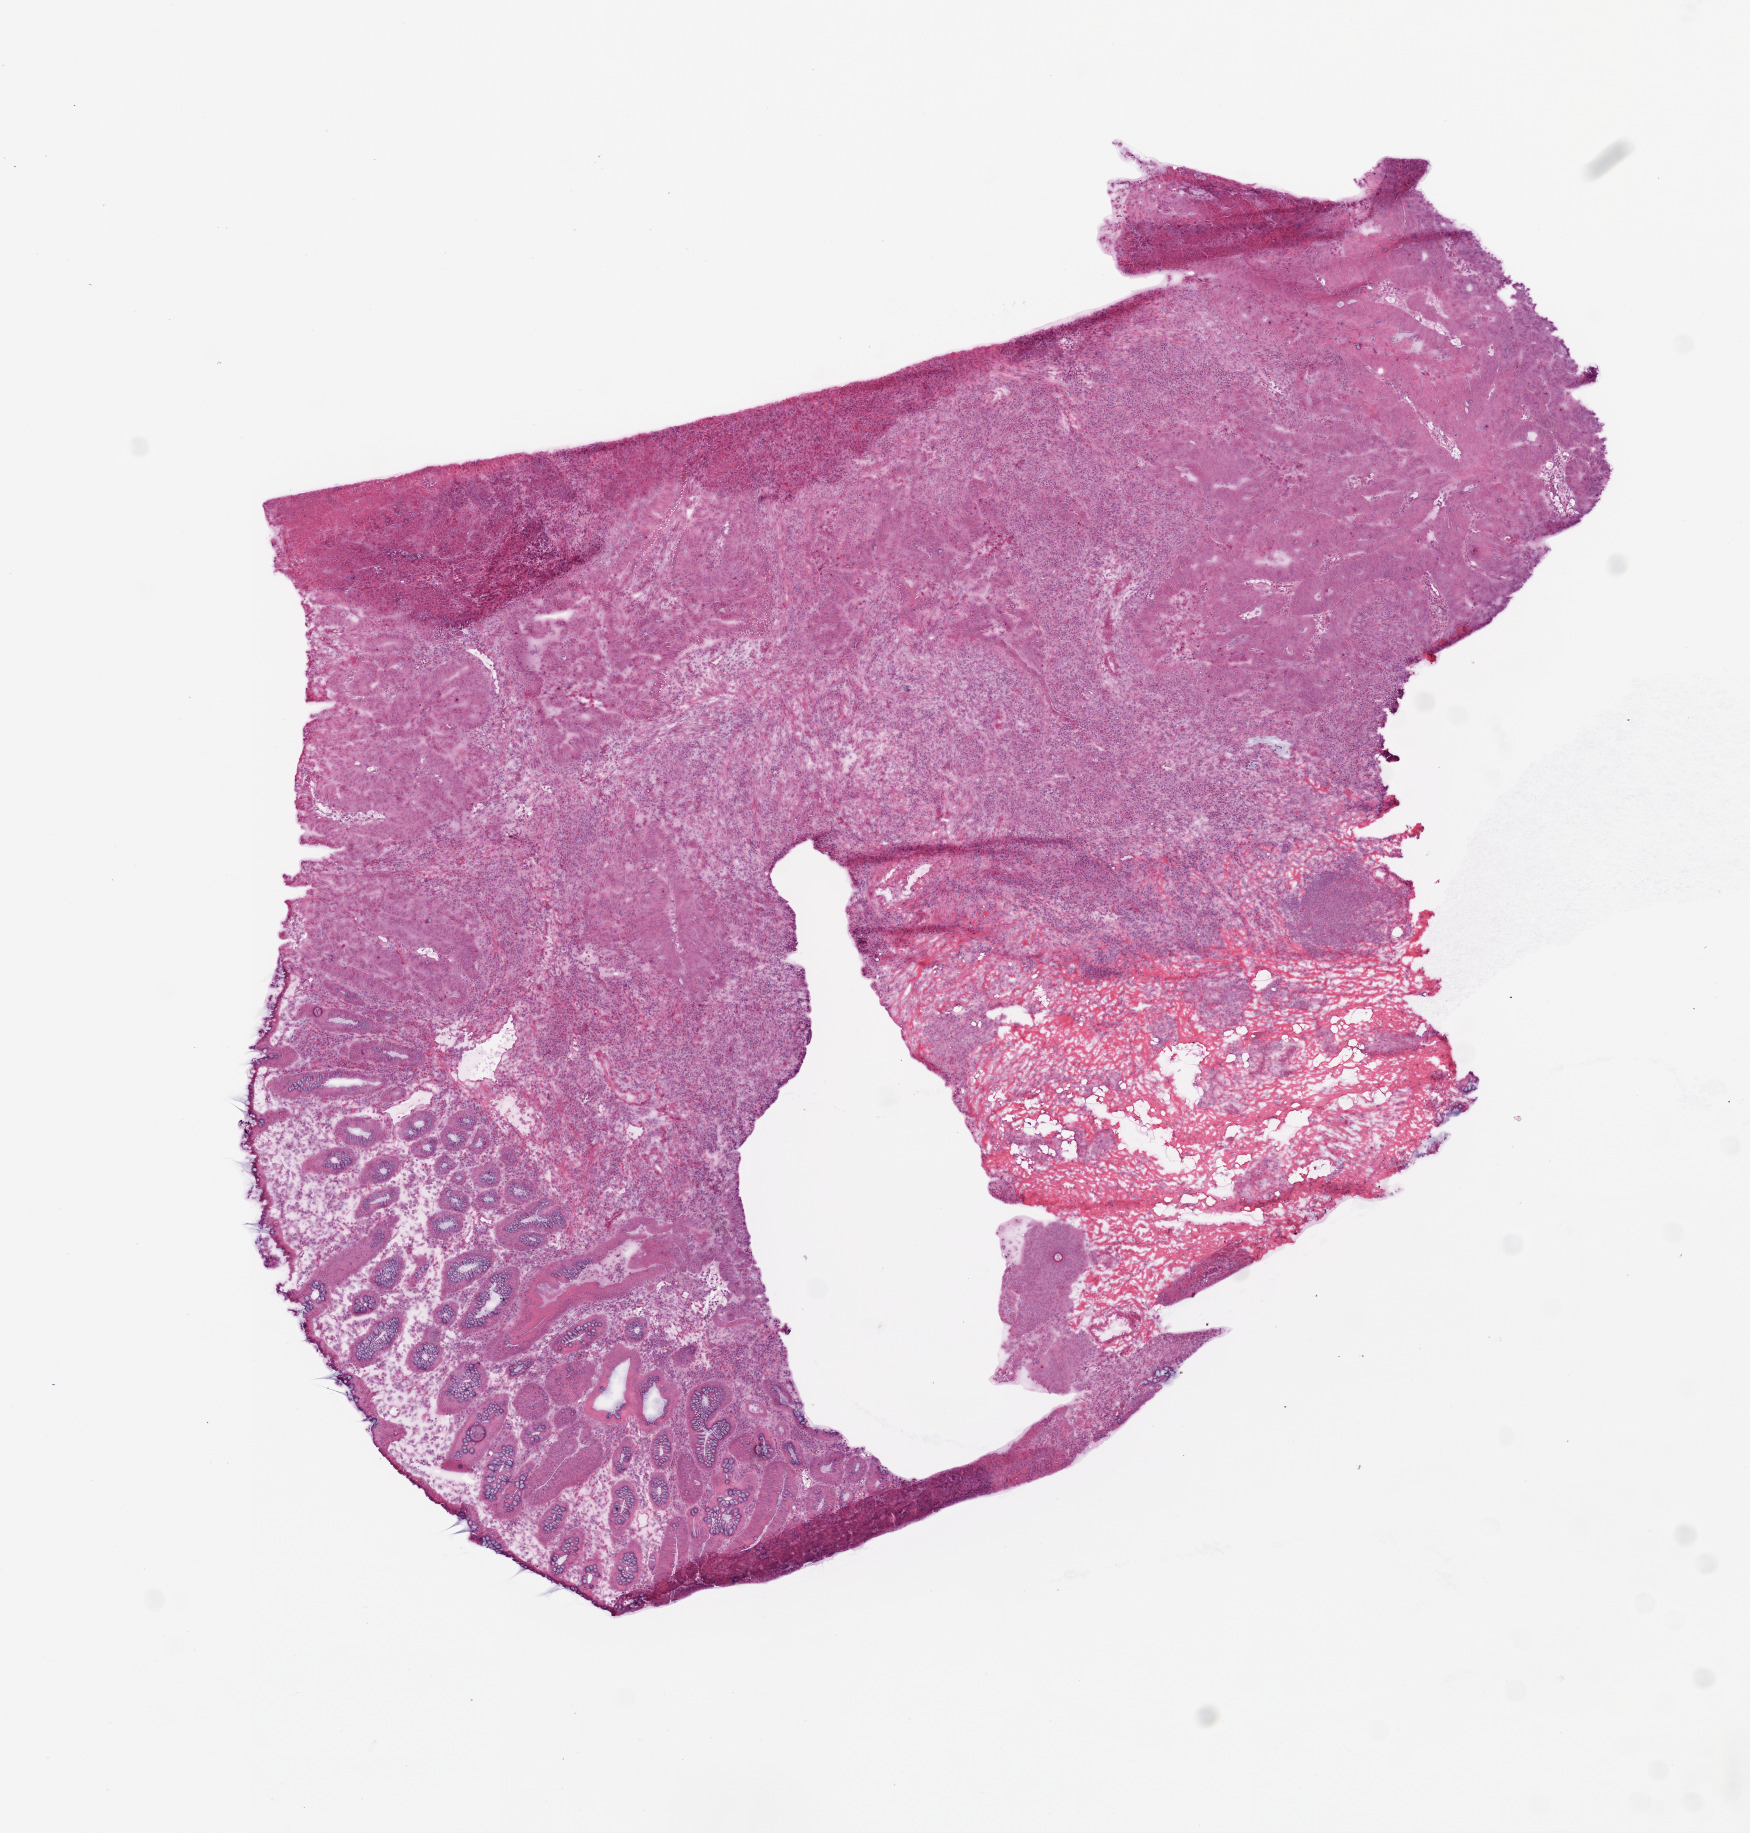
Digitized H&E-stained tissue section (whole slide), a low-resolution overview of the entire scanned area, about 7.0 x 7.4 mm (acquisition: 20x scan). Frozen section. Colon, primary tumour sample. Female patient; age at initial diagnosis 78 years. Pathologist review of this section (percent, as recorded): tumour cells 60%, tumour nuclei 70%, normal cells 20%, stromal cells 15%, necrosis 5%.
Histologic diagnosis: Adenocarcinoma, NOS. AJCC pathologic stage: I (6th edition). Lymph nodes positive (case pathology): 0 of 31 examined.